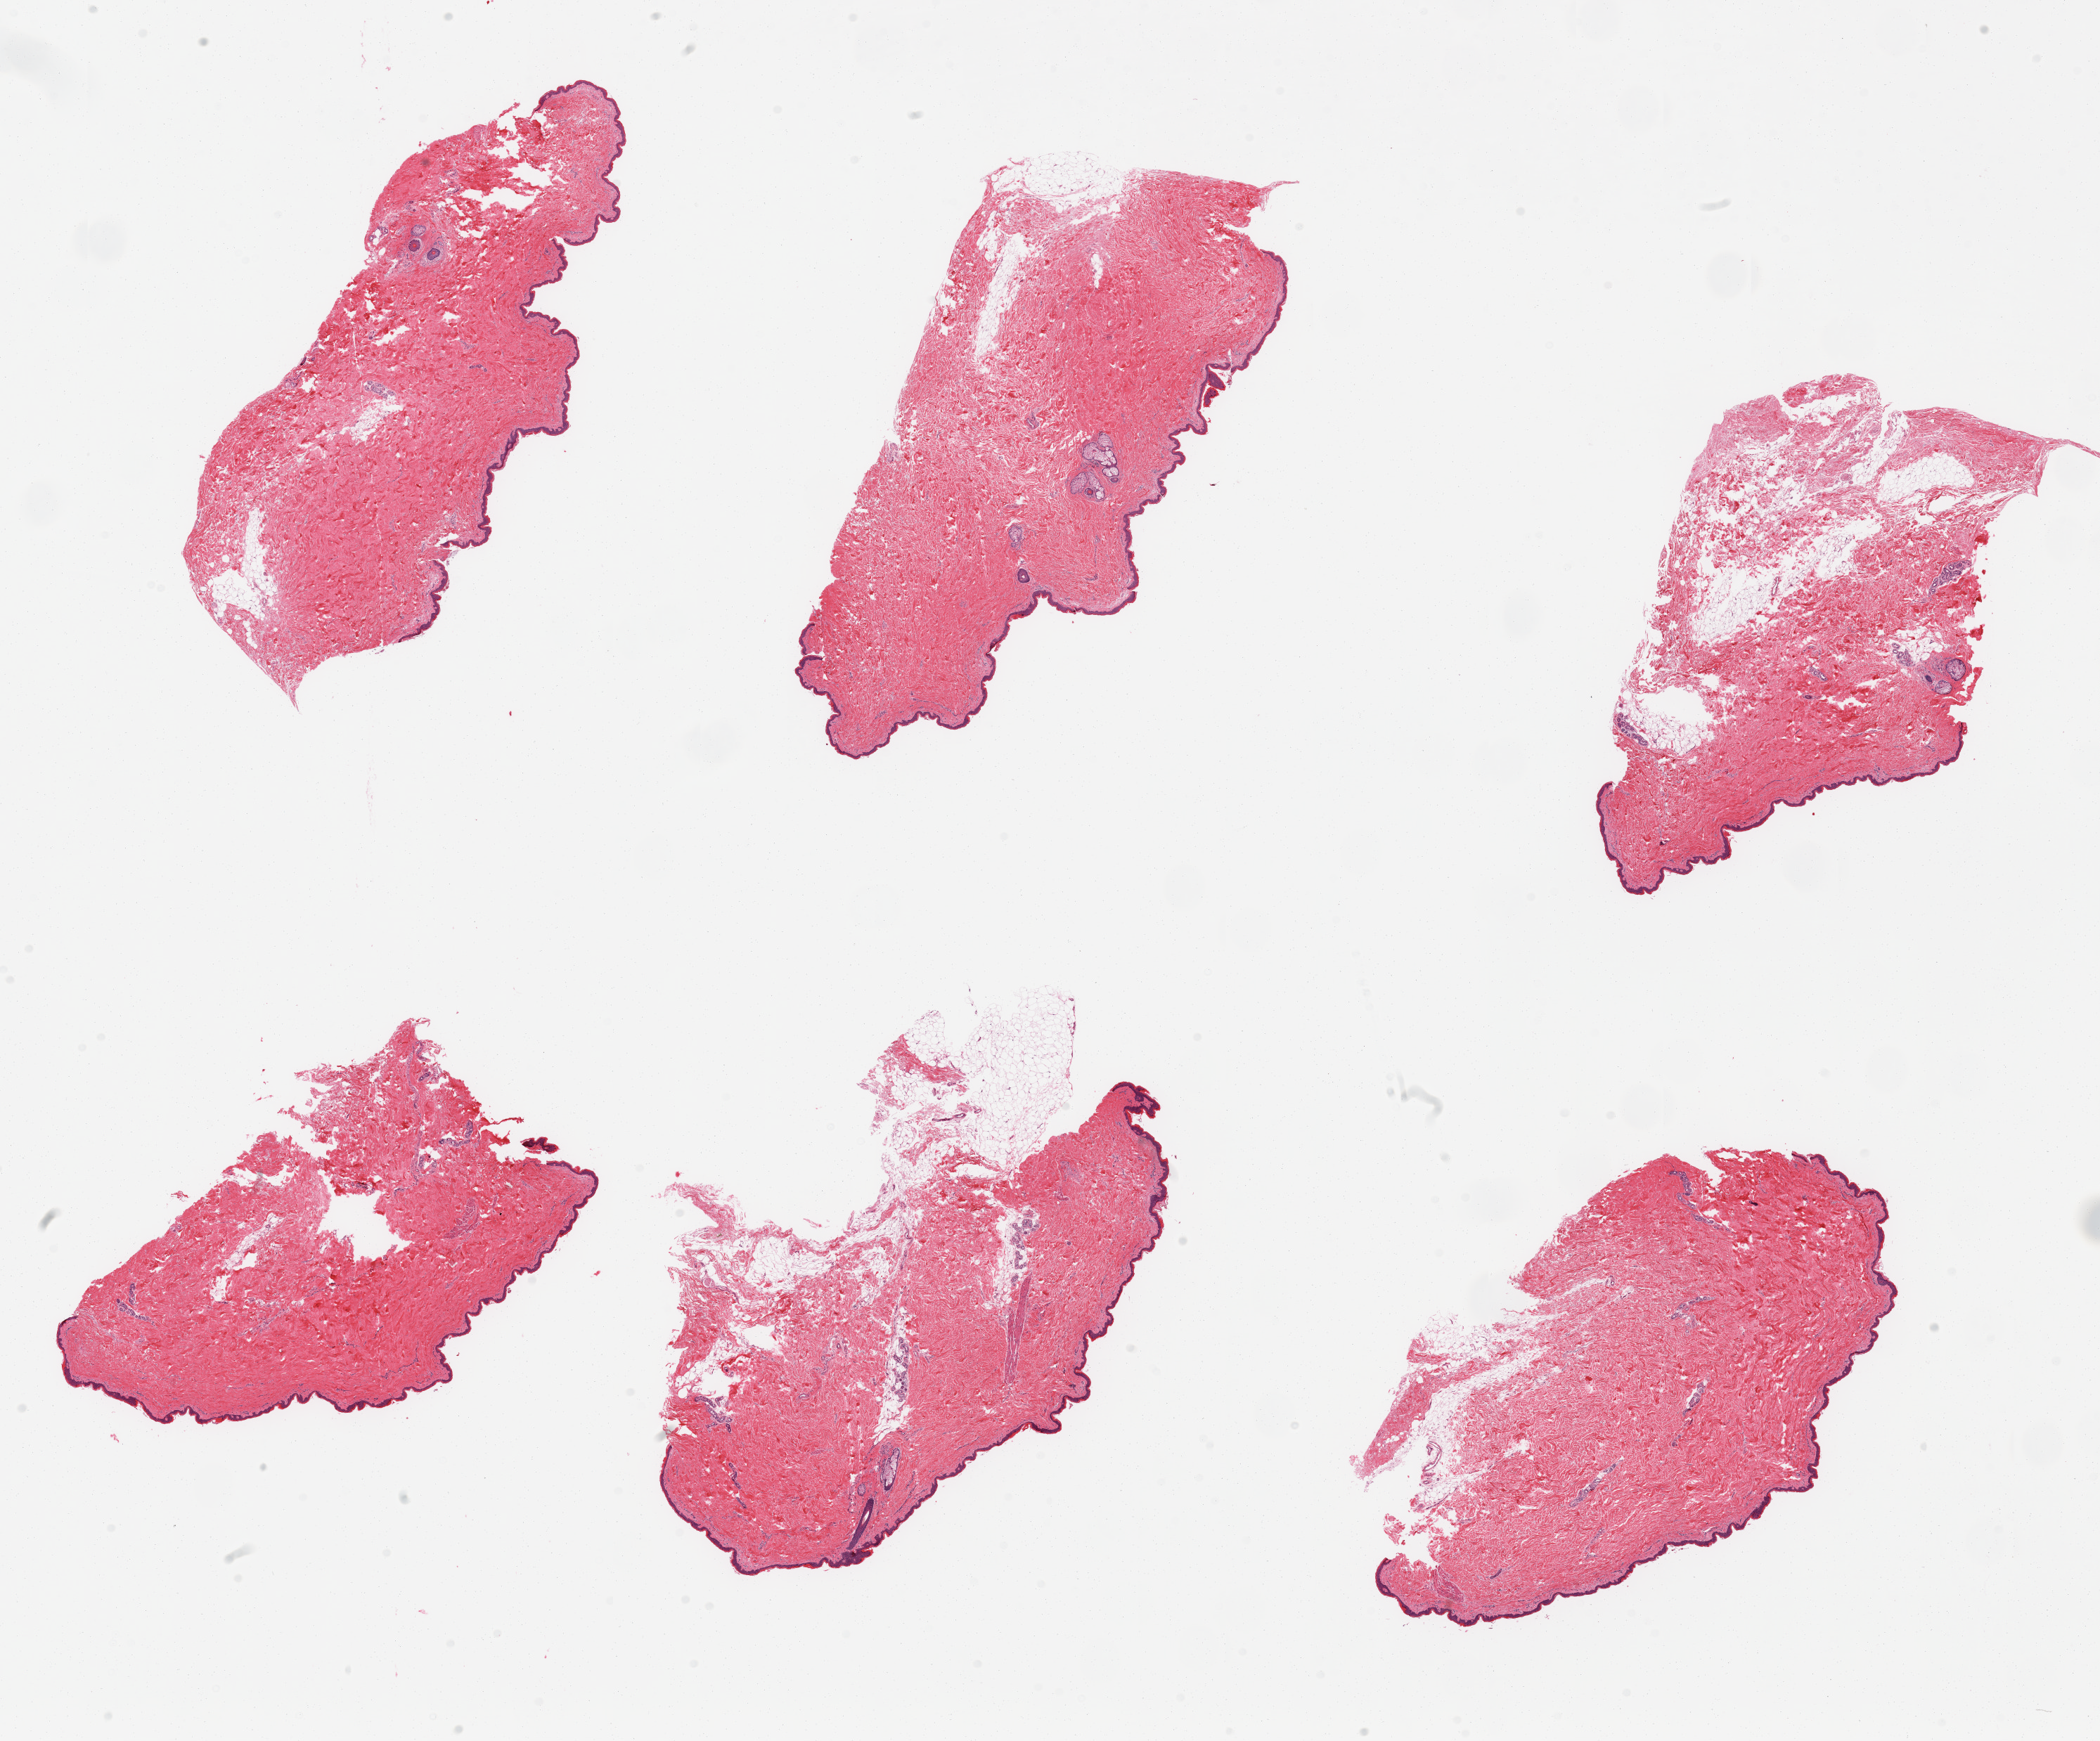
Whole-slide image, H&E stain, brightfield, a low-resolution overview of the entire scanned area, about 23.6 x 19.6 mm. PAXgene-fixed paraffin-embedded (PFPE) section. Section of skin of suprapubic region (target tissue). Tissue donor sample.
Review note (as recorded): 6 pieces, some with attached and internal fat from 10-20%.